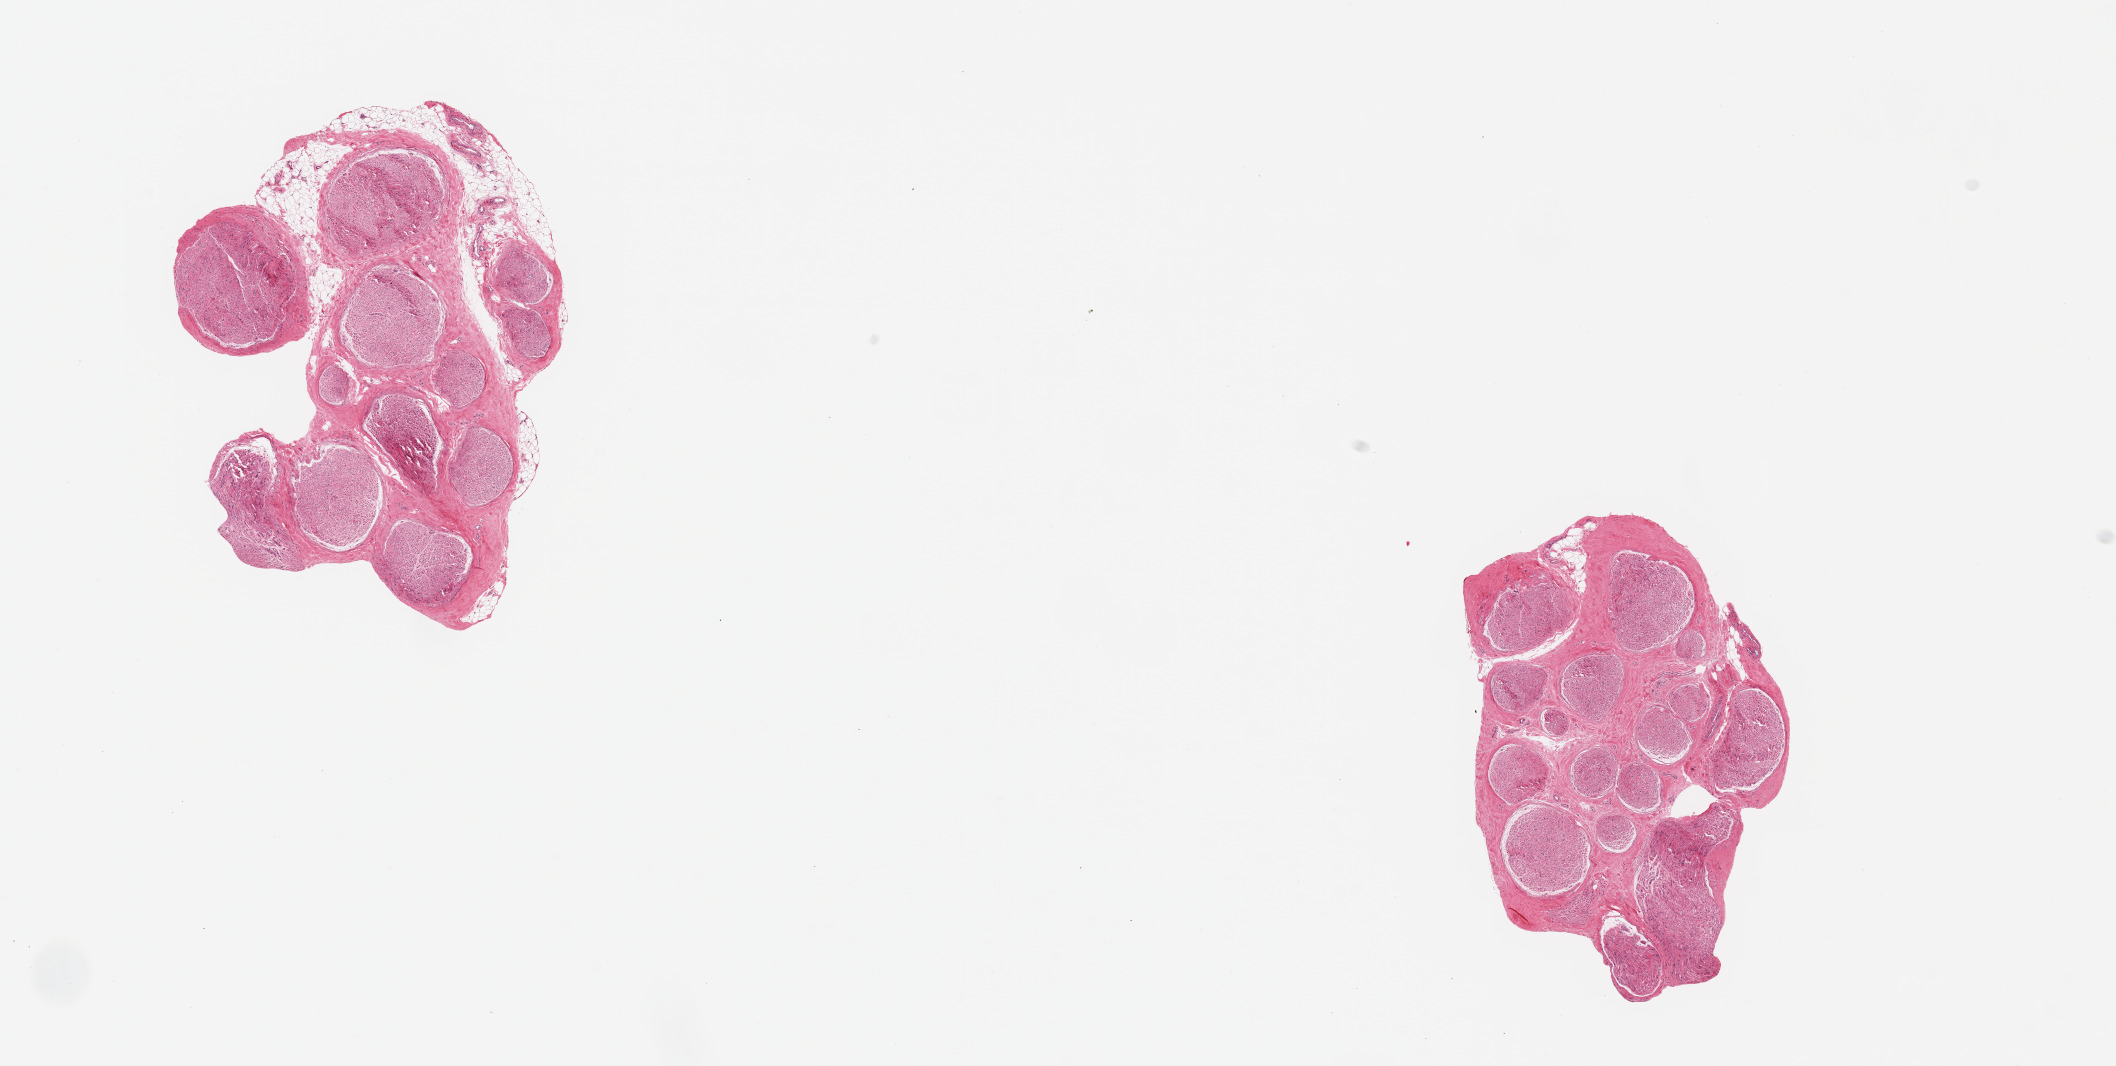
Digitized haematoxylin and eosin-stained section — shown as a low-resolution overview of the whole scanned area (about 16.7 x 8.4 mm); PAXgene-fixed paraffin-embedded (PFPE) section; target tissue: tibial nerve; tissue donor sample. Male donor.
* reviewer comment on this tissue sample: 2 pieces, minimal adherent fat